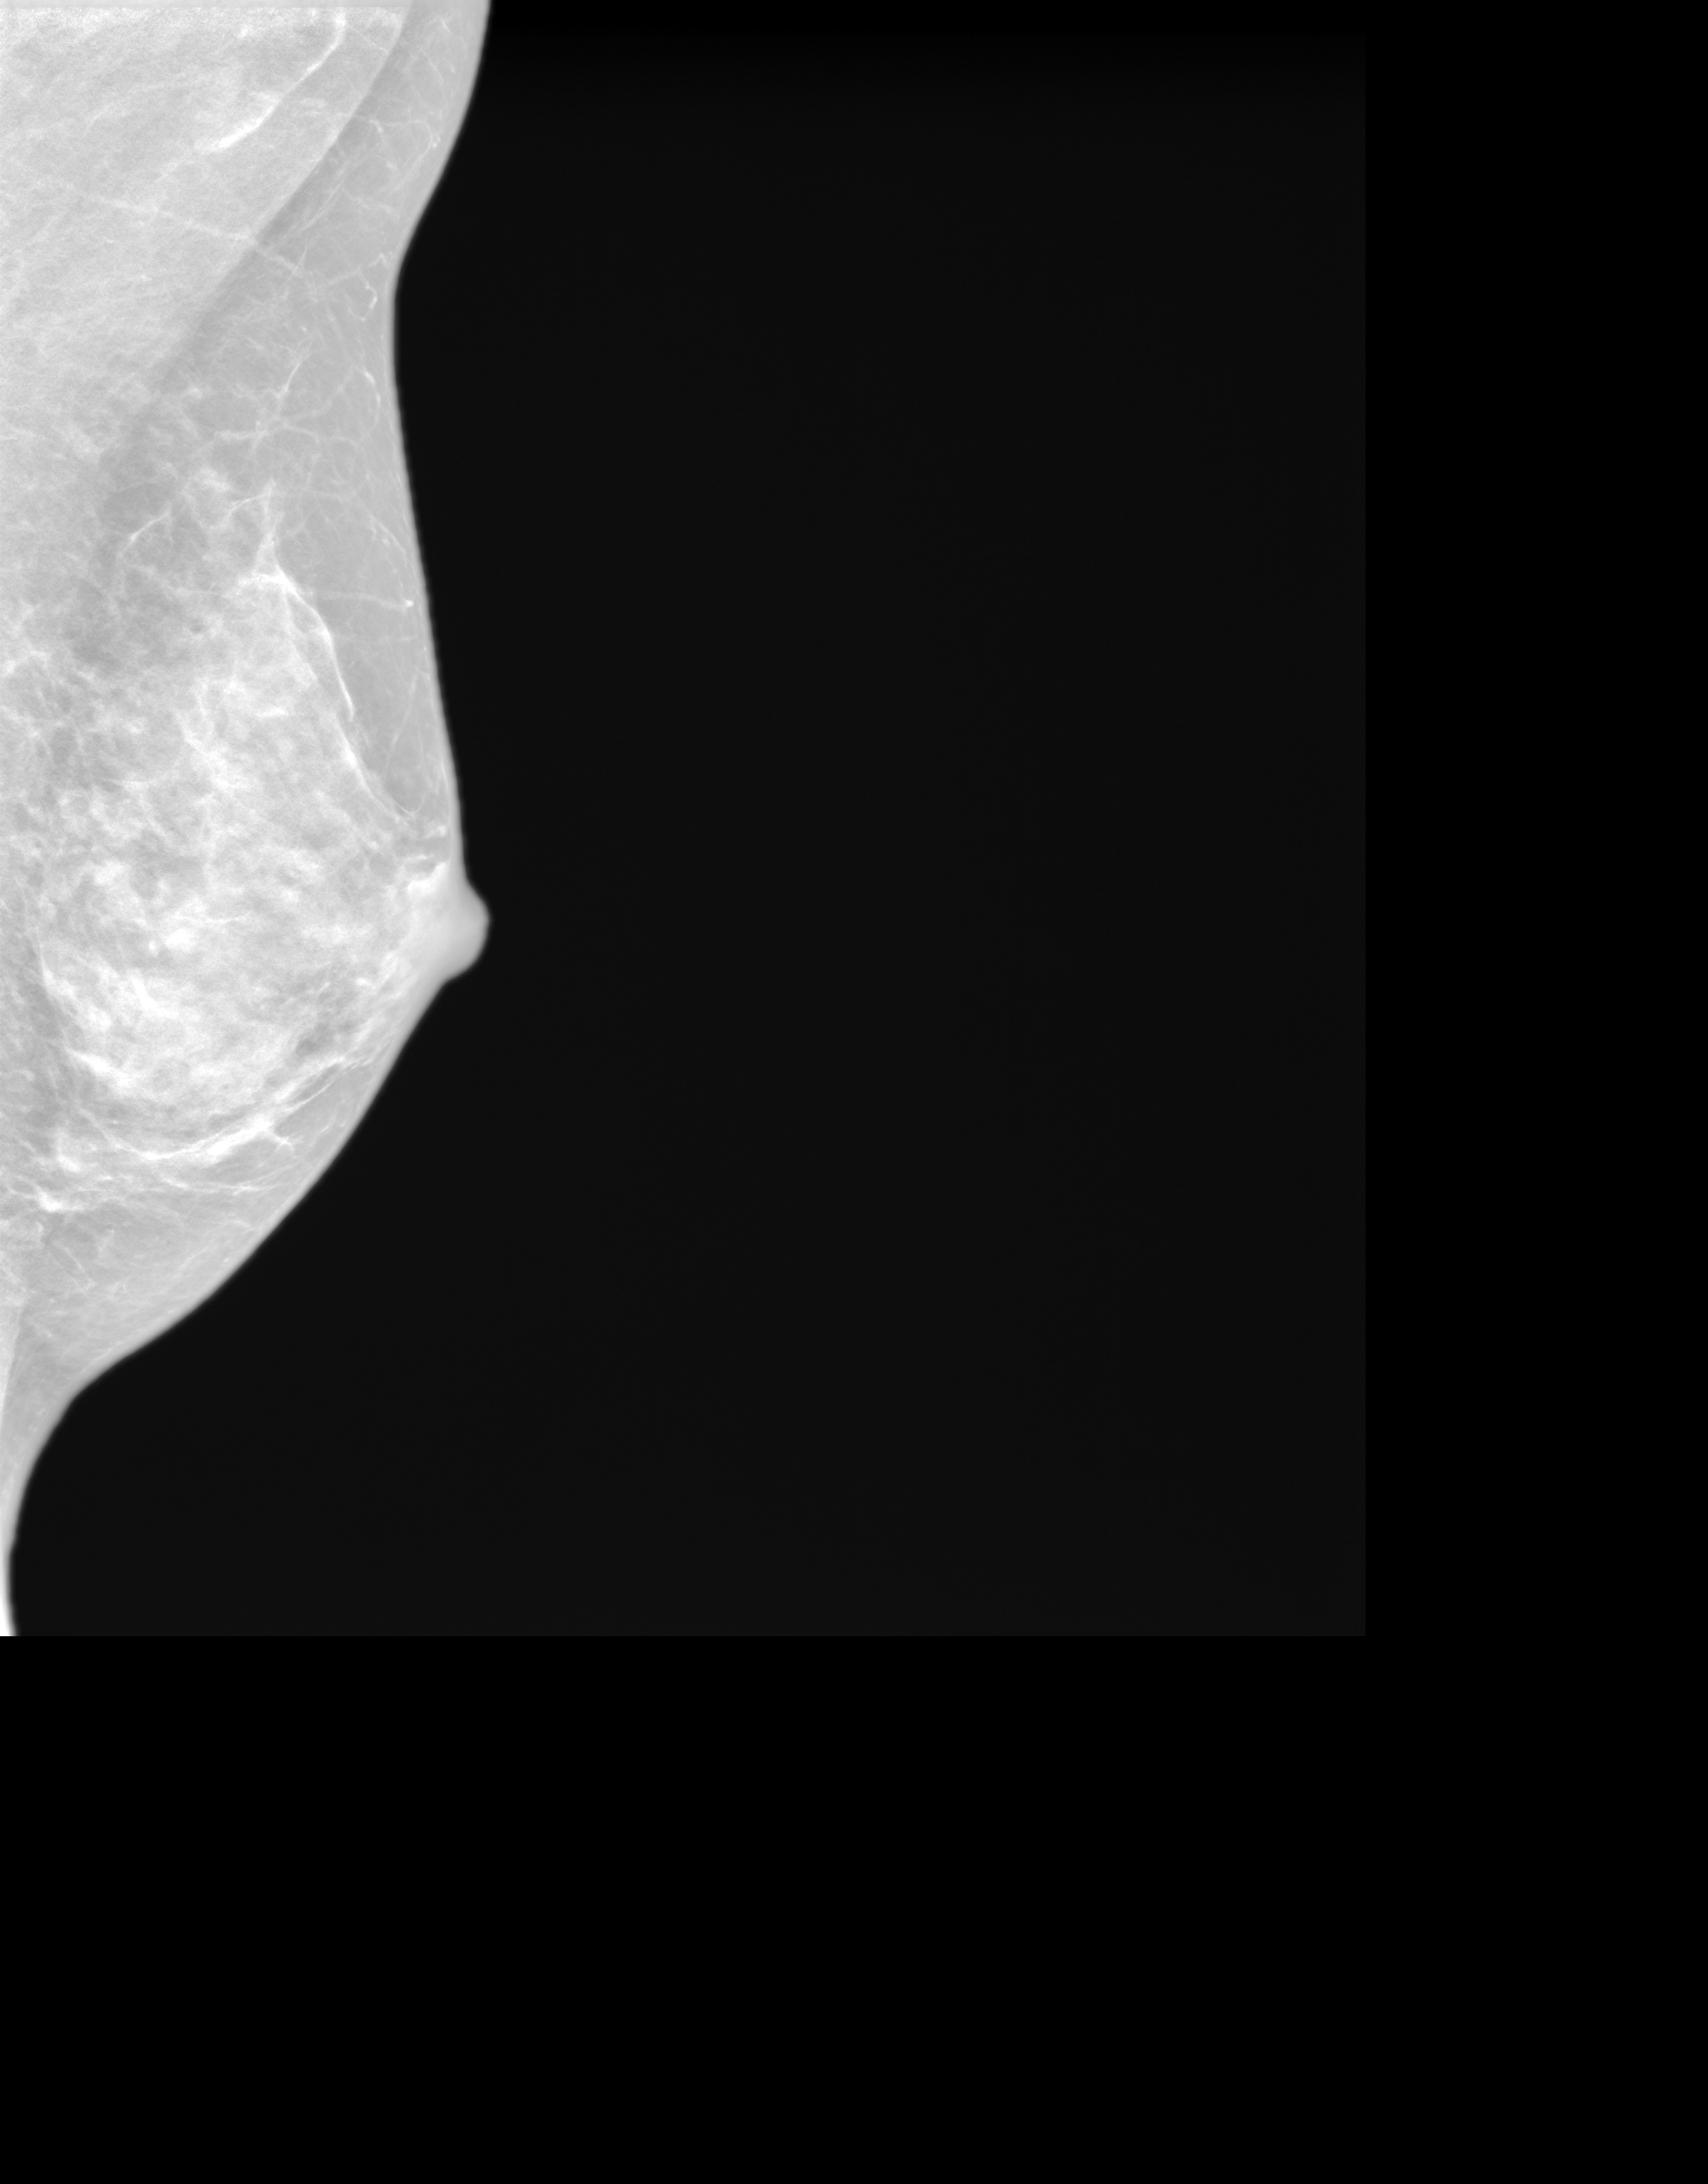
Annual screening mammography examination. Patient aged 56 years (female).
Image type: synthesized 2-D view from tomosynthesis. Breast: left. Projection: medio-lateral oblique projection.